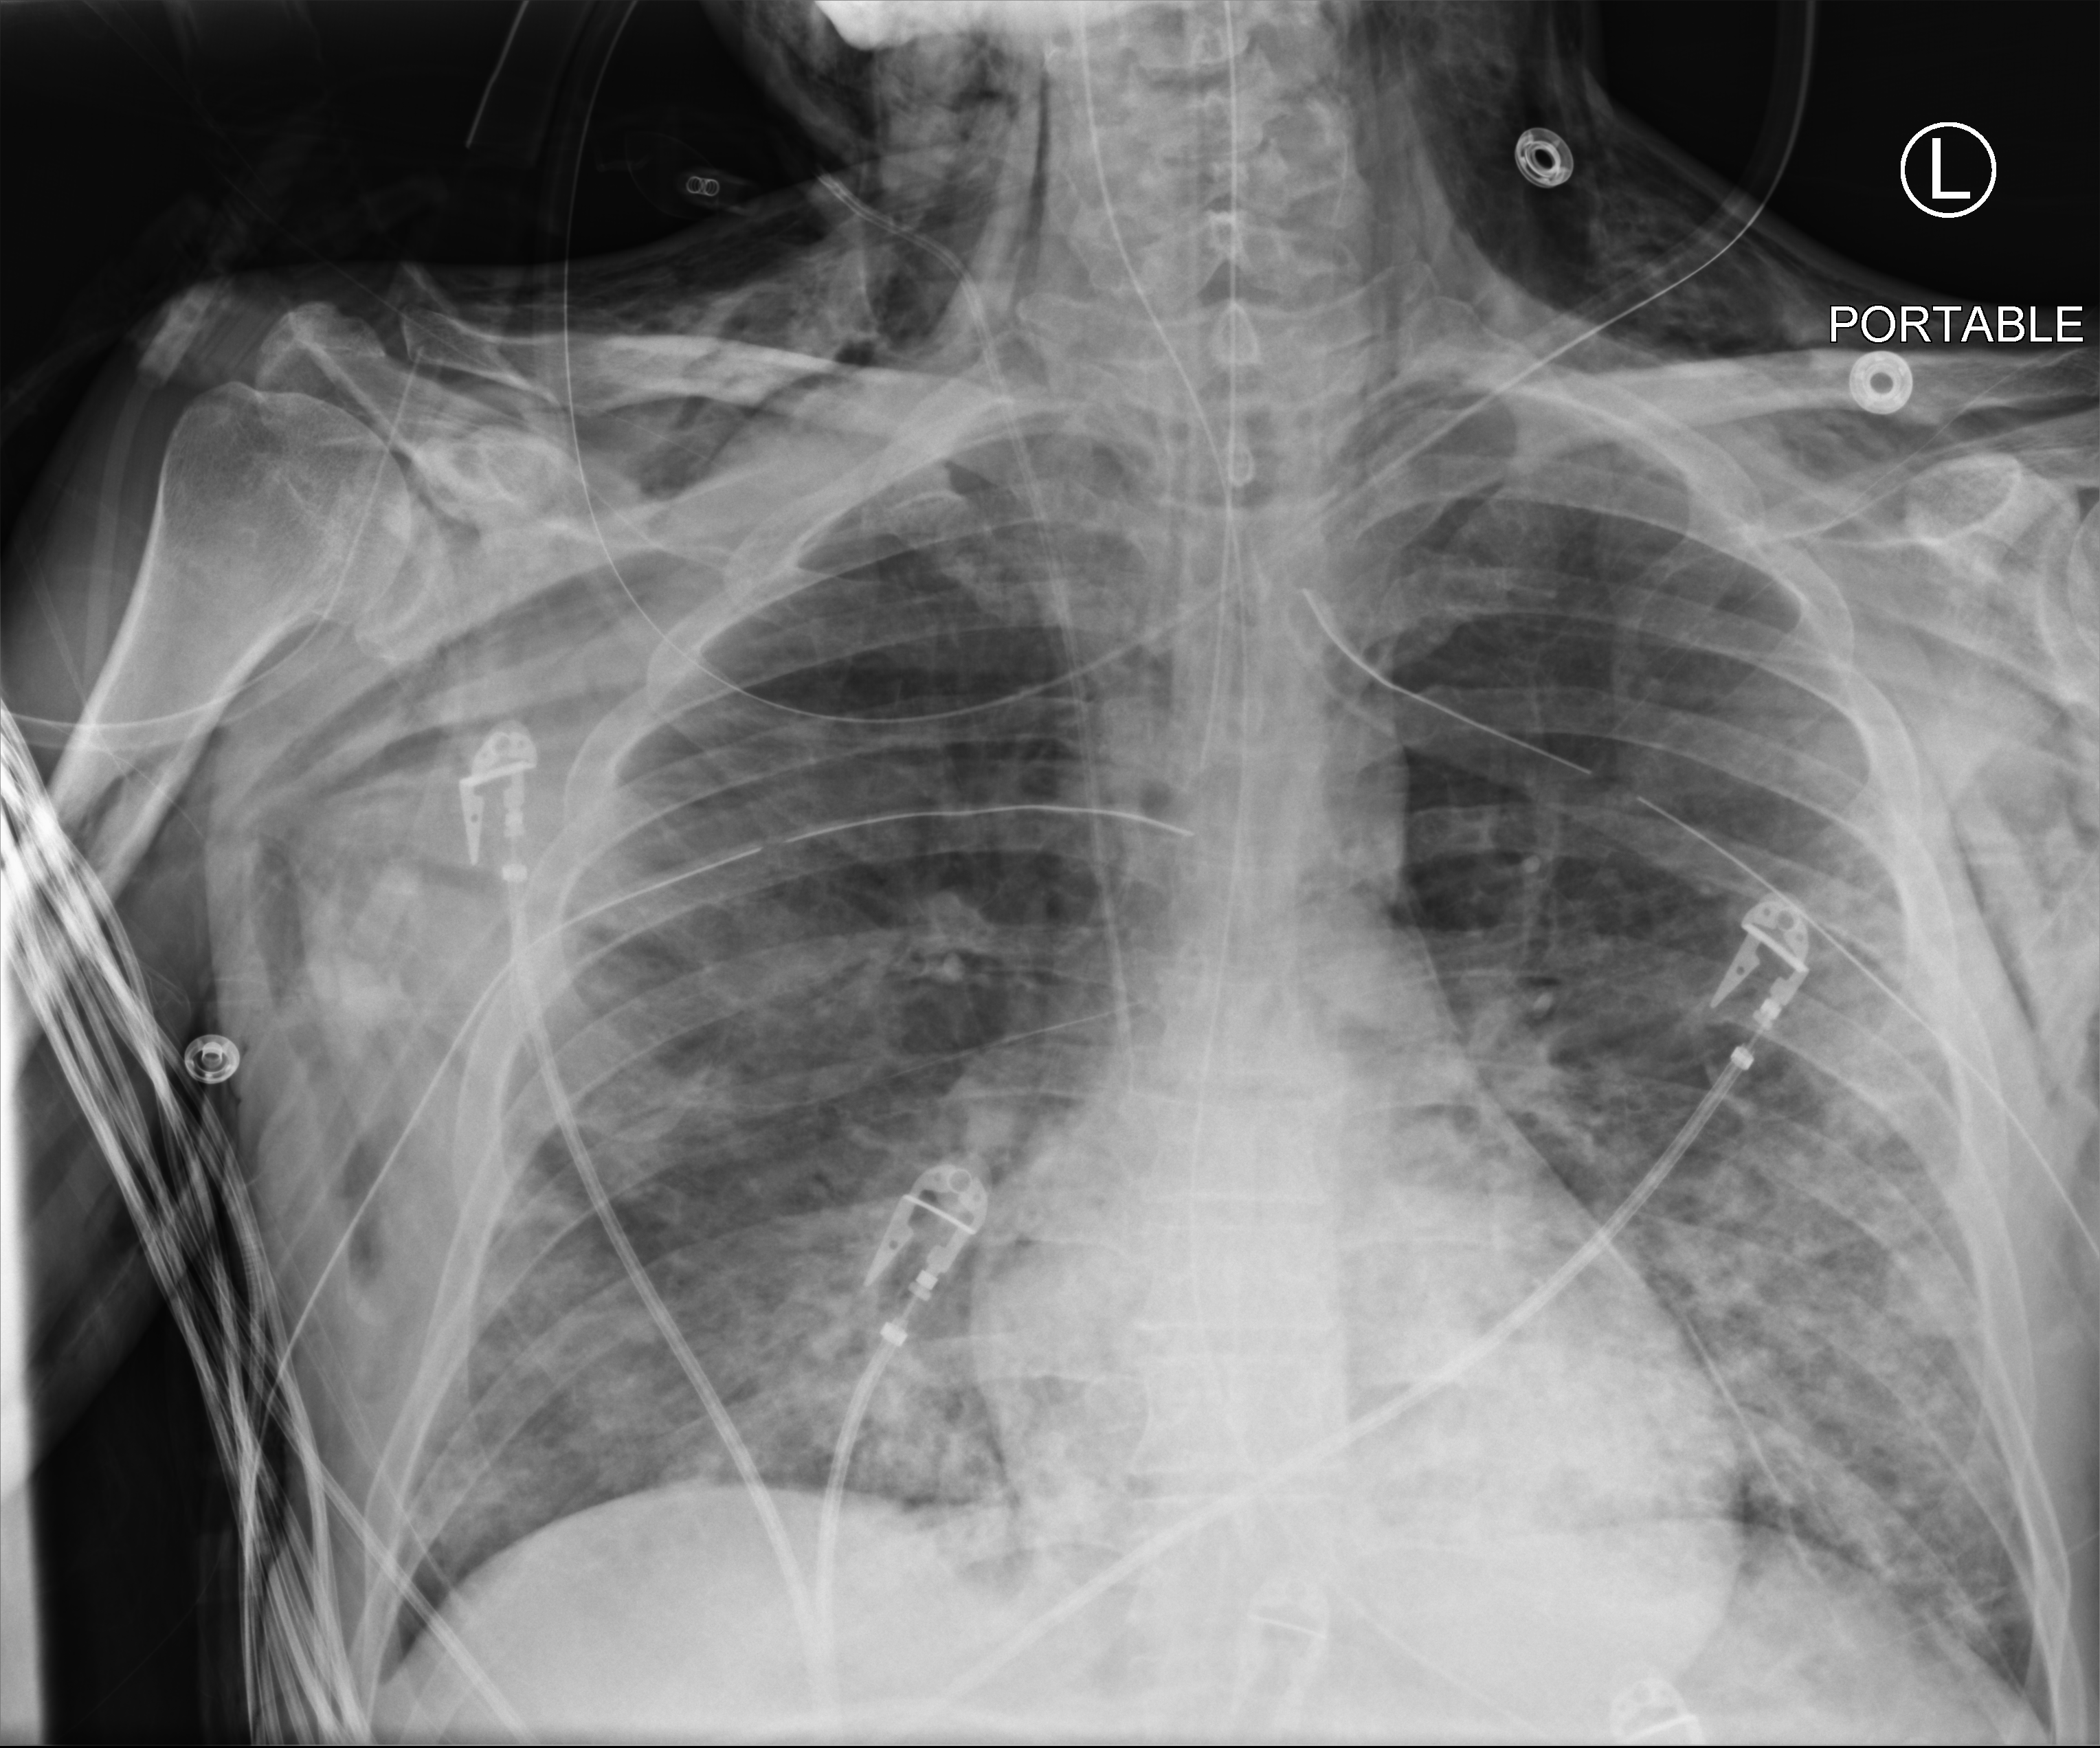
Bedside chest radiograph (computed radiography); anteroposterior (AP) projection. Patient hospitalised with COVID-19; male, aged 18–59 years.
Admission-level facts for this patient (not findings on this image; timing relative to this image not recorded): chronic kidney disease (admission record): no.